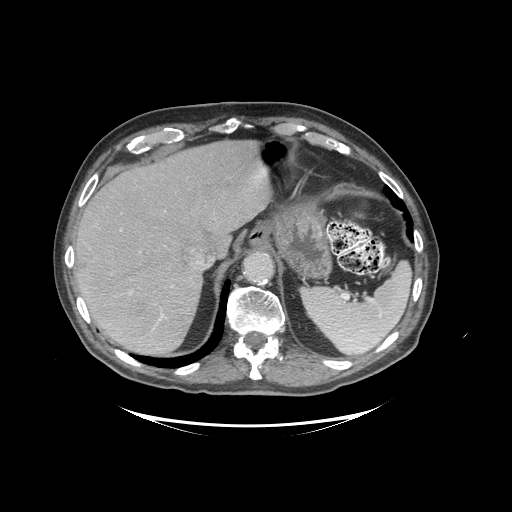
Contrast-enhanced abdominal CT (liver protocol), one axial slice; position 76 of 99 along the scan axis; 140 kVp; soft-tissue window (W 400 / L 40 HU); 512 × 512 image matrix, field of view 460 × 460 mm. From the clinical record (not read from this slice): diagnosis: hepatocellular carcinoma (patient treated with transarterial chemoembolisation; whether this scan precedes or follows treatment is not stated here); TNM stage (as recorded): Stage-I; Child-Pugh class: A; tumour differentiation: moderately differentiated.
Annotated regions visible in this slice (semi-automatically segmented with operator editing):
- liver parenchyma outside the tumour (the mass and vessels are separate outlines, so this box may not span the whole liver): bounding box <74,140,270,354> (left, top, right, bottom; pixels)
- liver vessels: <130,169,266,321>